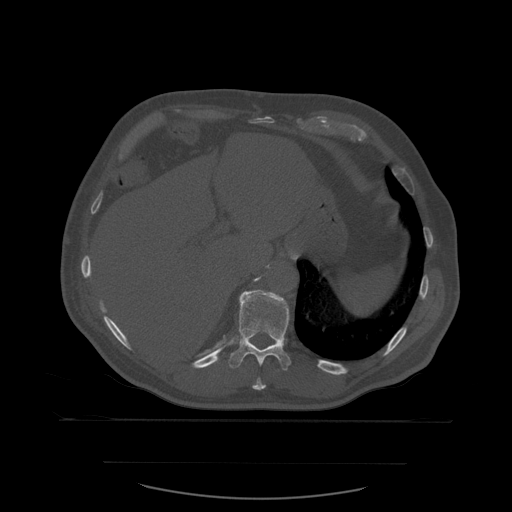
CT including the spine, one axial slice; slice 297 of 590 in the series (ordered by position); bone window (W 1800 / L 400 HU); 1.25 mm slice thickness; 512 × 512 image matrix, field of view 479 × 479 mm. Patient age 71 years. Case-level facts recorded for this patient, not image findings: primary cancer: lung; vertebrae with lytic lesions (as recorded): T1, T2, L5, S1.
Annotated regions visible in this slice (semi-automatic segmentation, software-assisted and operator-edited):
- T10 vertebra: bounding box (x1, y1, x2, y2) in pixels: (253, 378, 267, 391)
- T11 vertebra: (229, 290, 292, 371)